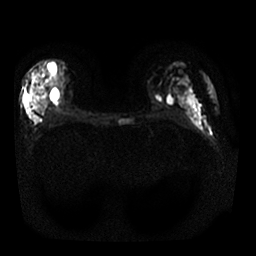
Breast MRI, one axial slice; diffusion-weighted series; image 2 of 4 stored at this slice position (different b-values; order by instance number); 1.5 T; 256 × 256 image matrix. Female patient.
Structures marked on this image (outlined manually by an expert reader):
- tumour on diffusion-weighted imaging: bounding box [x1, y1, x2, y2] px = [29, 100, 42, 115]